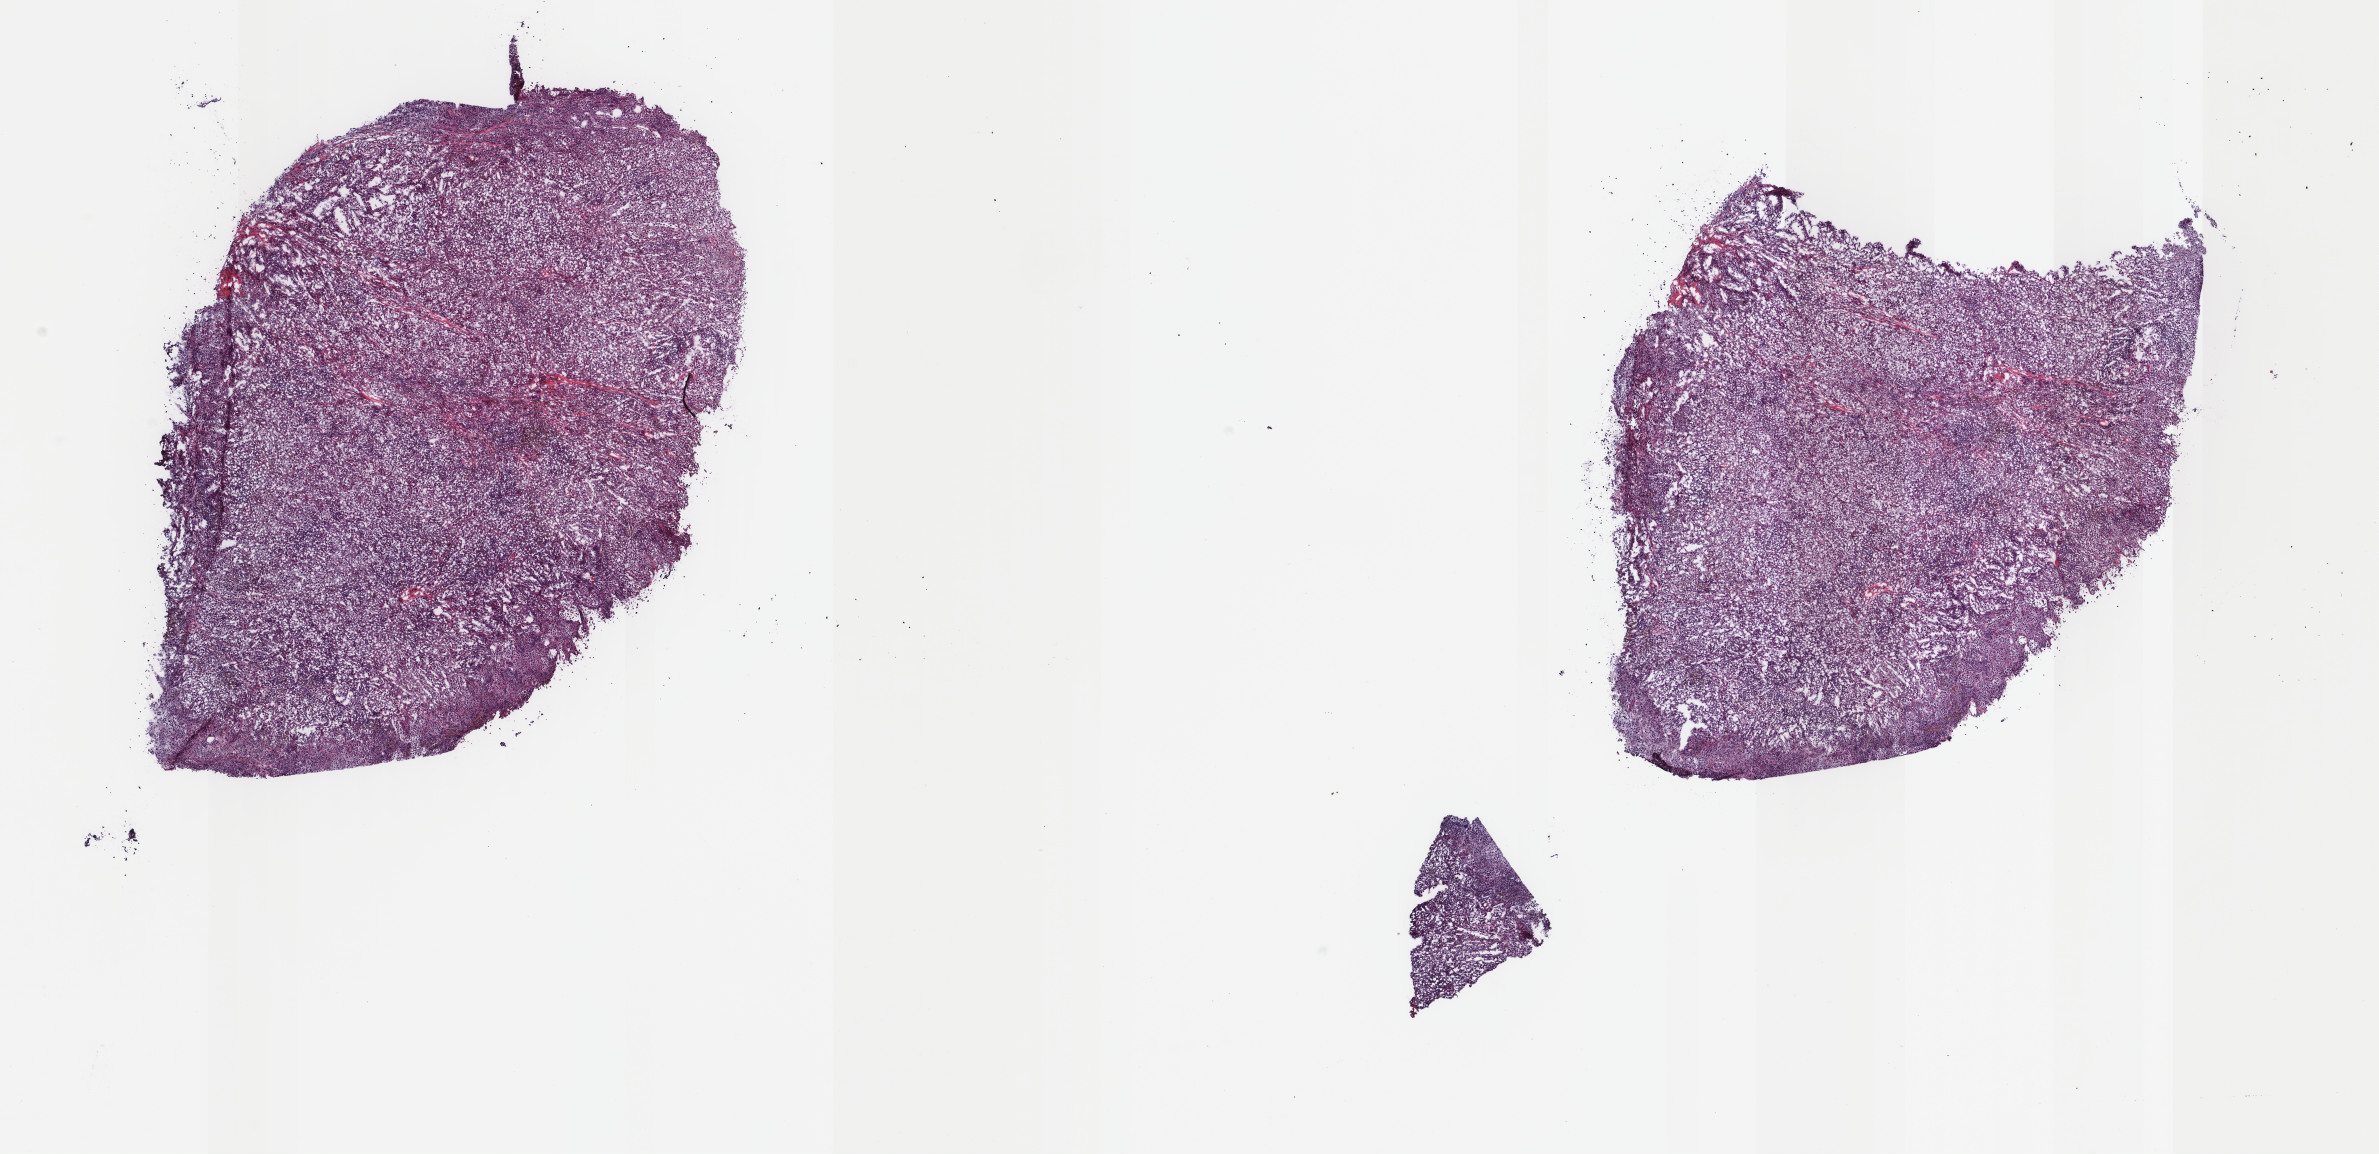
Whole-slide histology image, H&E, shown as a low-resolution overview of the whole scanned area (about 18.9 x 9.2 mm, from a 40x scan); frozen section from the top of the tissue portion; metastatic tumour sample. Patient: male, age at initial diagnosis 54 years. Composition of this section per pathologist review: tumour cells 95%, tumour nuclei 90%, normal cells 0%, stromal cells 5%, necrosis 0%. Infiltration values recorded for this section: lymphocyte infiltration 3%, monocyte infiltration 0%, neutrophil infiltration 0%.
This section: metastatic tumour tissue. Patient diagnosis: Malignant melanoma, NOS.